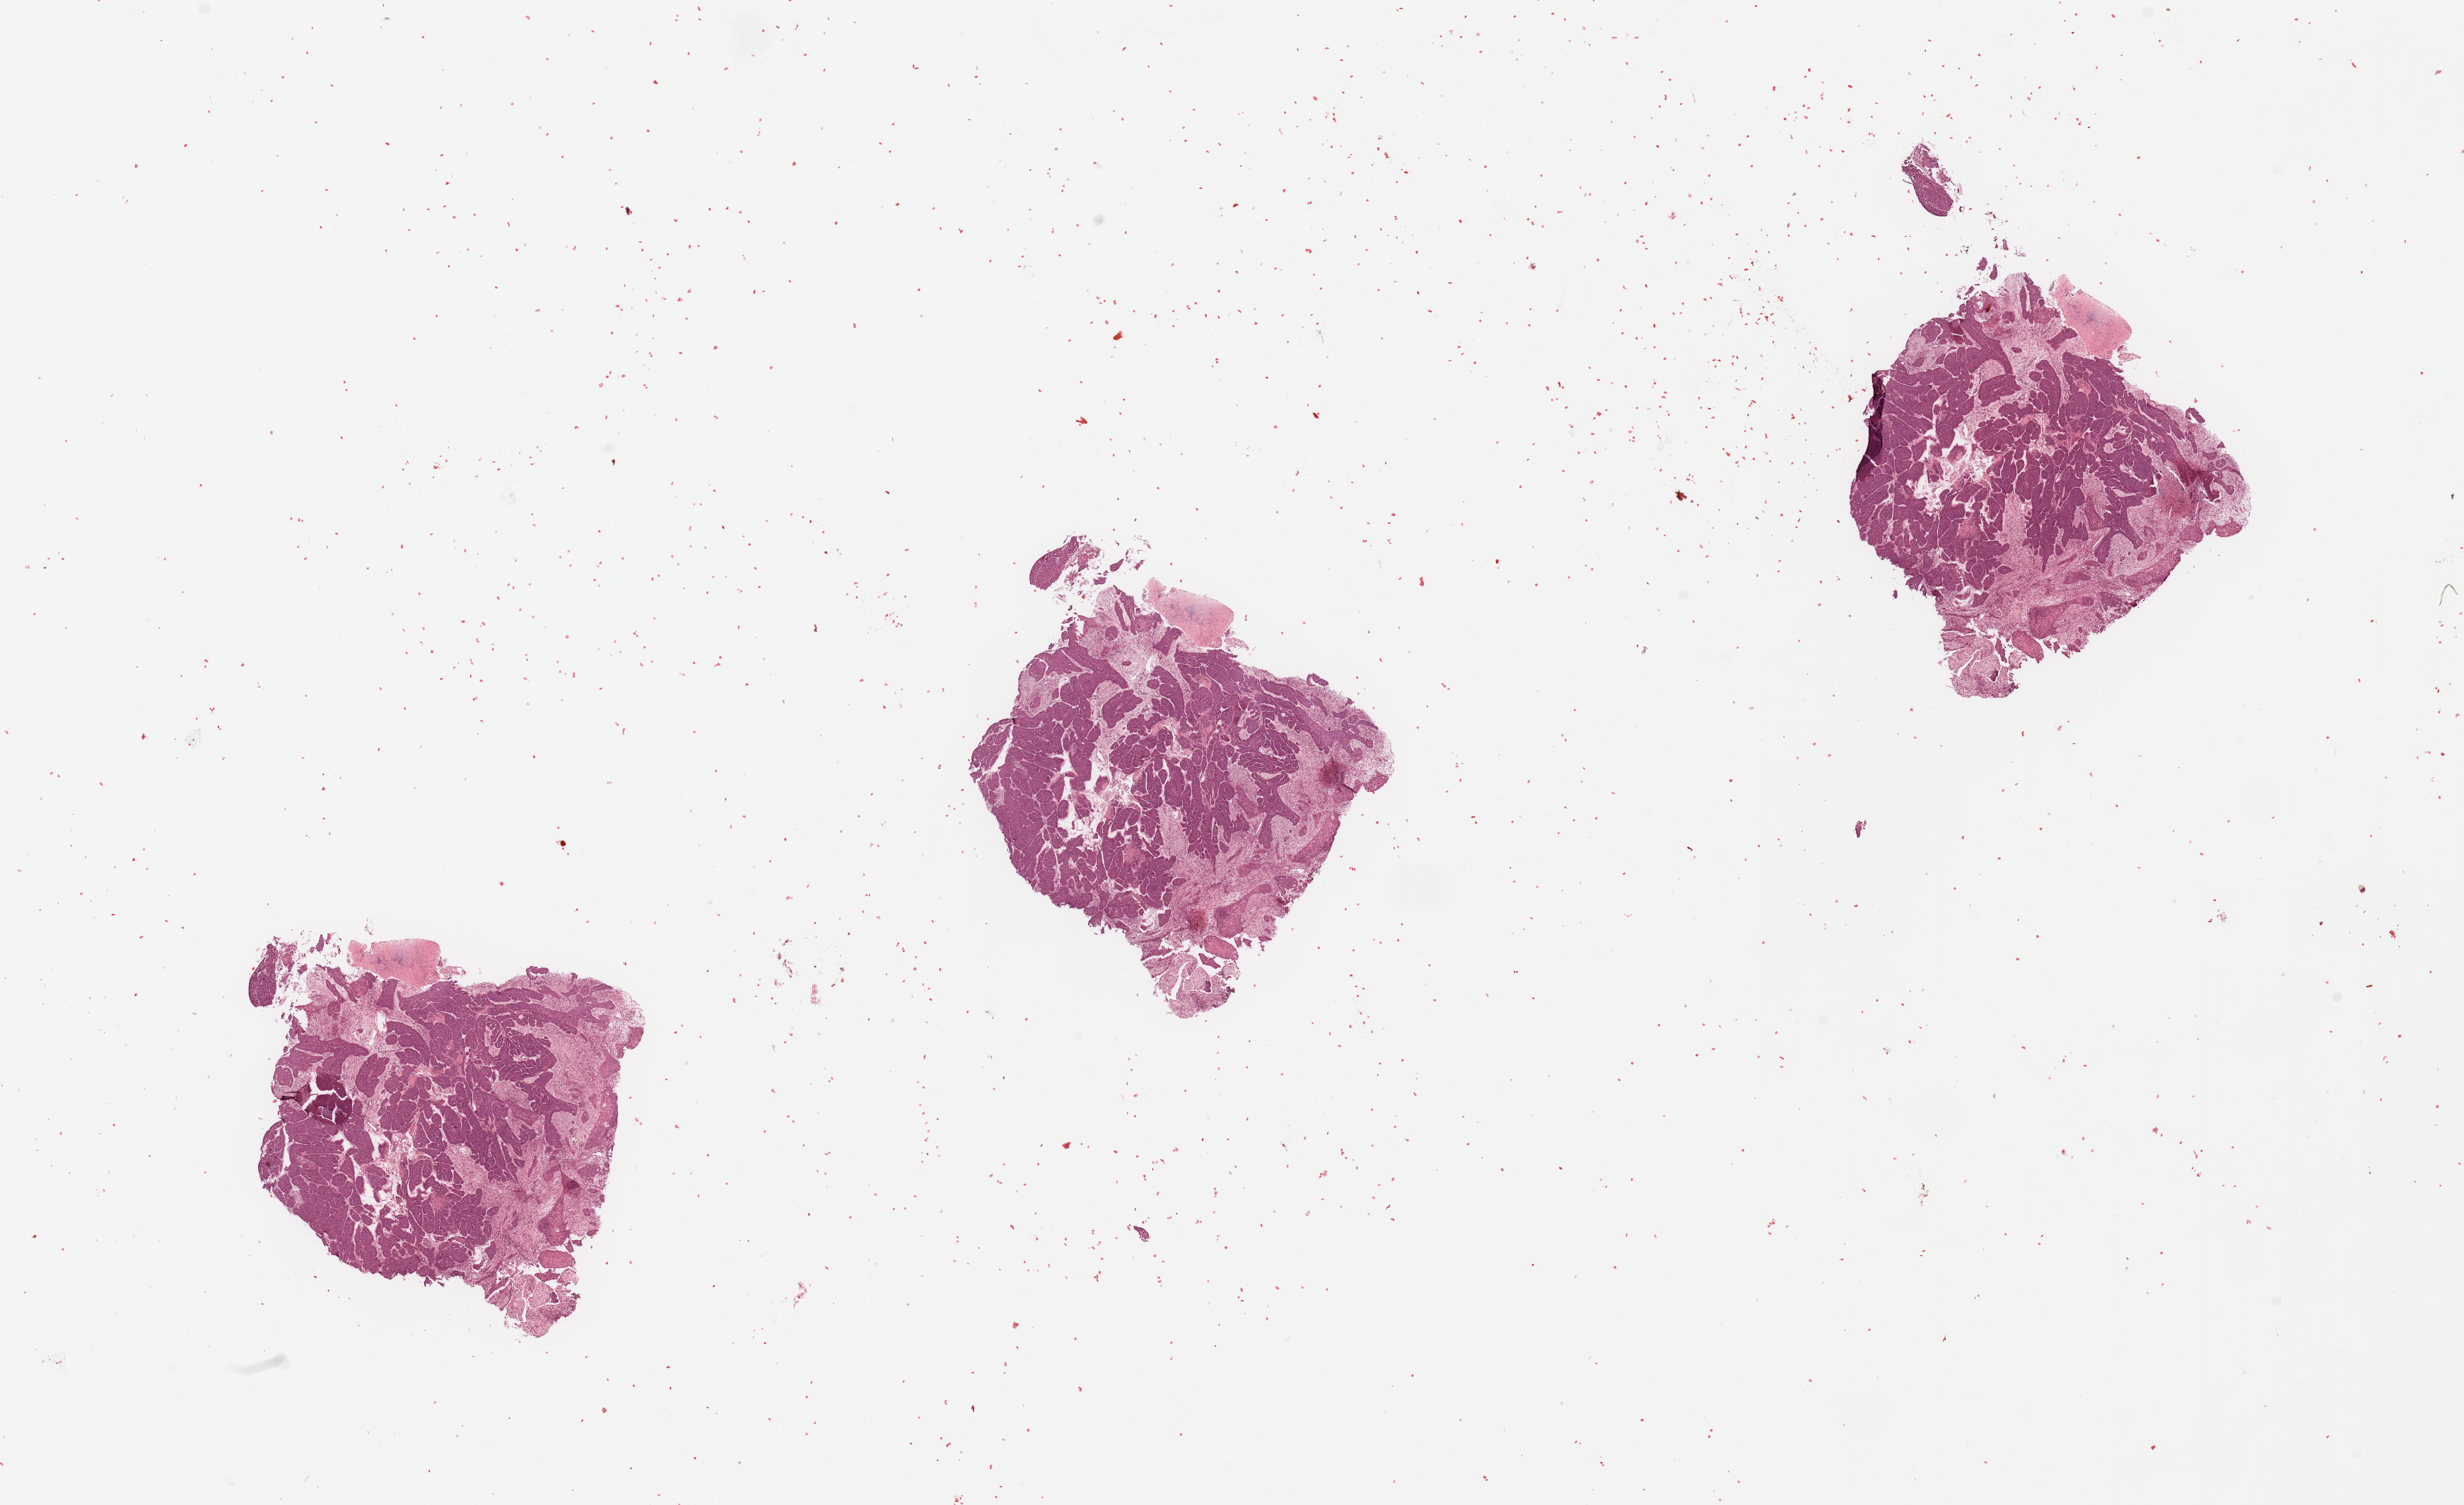
Digitized H&E-stained tissue section (whole slide) — low-resolution overview of the scanned area, about 27.6 x 16.8 mm. Tumour tissue sample, sampled site: larynx. Male, 62 y/o. Histologic grade: G2 (moderately differentiated). Composition of this section per pathologist review: tumour nuclei 80%, necrosis 5%.
Diagnosis: Squamous cell carcinoma, NOS (larynx, NOS). Primary tumour site (as recorded): hypopharynx. AJCC pathologic stage: III.